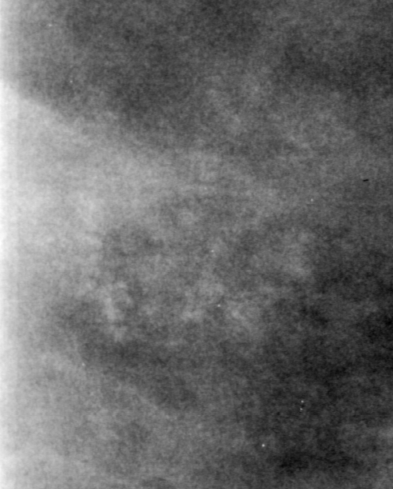
Cropped region of a digitized screen-film mammogram centred on a radiologist-marked abnormality, right breast, CC view, BI-RADS breast density category 4 (scale 1–4).
Finding: calcifications, morphology amorphous, distribution segmental; BI-RADS assessment category 4; pathology (as recorded): benign.